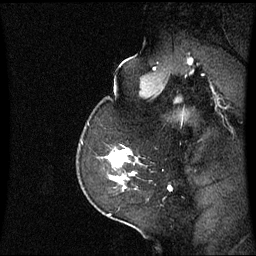
Breast MRI (dynamic contrast-enhanced), one sagittal slice. Position 47 of 60 along the scan axis. Dynamic contrast-enhanced series, image 2 of 3 at this slice position (ordered by acquisition). 1.5 T. TE 4.2 ms, TR 8.9 ms. 2.2 mm slice thickness. 256 × 256 image matrix, field of view 220 × 220 mm. Female patient, age 58 years. Case-level facts recorded for this patient, not image findings: setting: breast cancer imaged before/during neoadjuvant chemotherapy; receptor status: triple-negative.
Structures marked on this image (semi-automatic segmentation, software-assisted and operator-edited):
- analysis volume of interest (the breast-tissue region the enhancement analysis was run in; not a lesion): bounding box [x1, y1, x2, y2] px = [98, 148, 139, 191]
- tumour enhancement mask (voxels above the 70 % enhancement threshold inside the analysis volume of interest): [108, 148, 135, 183]